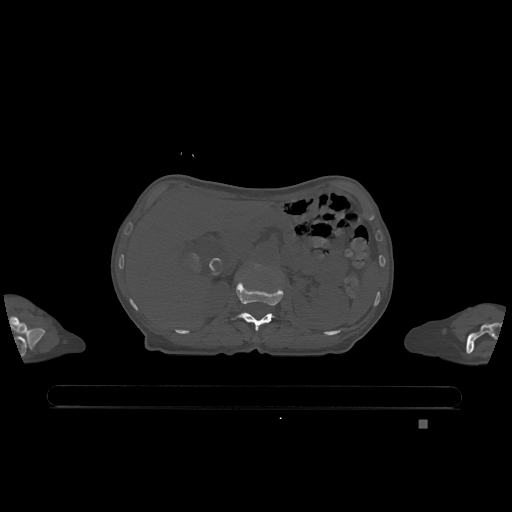
CT including the spine, one axial slice; slice 468 of 1317 in the series (ordered by position); bone window (W 1800 / L 400 HU); 512 × 512 image matrix, field of view 500 × 500 mm. Female patient, age 74 years. From the clinical record (not read from this slice): primary cancer: lung.
Outlined on this slice (semi-automatic segmentation, software-assisted and operator-edited):
- L1 vertebra: bounding box <225,281,284,331> (left, top, right, bottom; pixels)